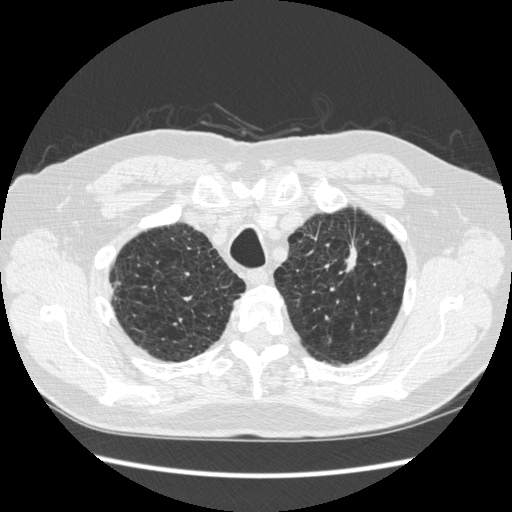
Chest CT (low-dose screening protocol), one axial image, third screening round (two years after baseline), lung window (W 1500 / L -600 HU), 1.25 mm slice thickness, standard (soft-tissue) reconstruction kernel (STANDARD). Male, age 70 years at enrolment.
- Lesion marked by an expert reader, box from (x=323, y=223) to (x=375, y=288) px.
- The screening reader recorded 2 non-calcified nodules or masses ≥4 mm on this exam (left upper lobe, right lower lobe); which of them this box marks is not recorded.
- Participant outcome: lung cancer diagnosed 92 days after this screen — squamous cell carcinoma, NOS, left upper lobe, moderately differentiated (G2), stage IA (AJCC 6th edition), 18 mm at pathology.